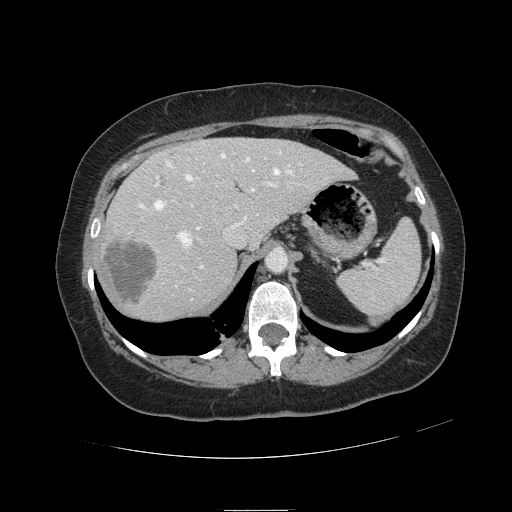
Contrast-enhanced abdominal CT, one axial slice; 120 kVp; intravenous contrast given; soft-tissue window (W 400 / L 40 HU); 2.5 mm slice thickness; 512 × 512 image matrix. Female patient, age 52 years. Case-level facts recorded for this patient, not image findings: diagnosis: colorectal cancer liver metastases, imaged before liver resection; multiple liver metastases: yes; largest metastasis: 6.3 cm; disease in both lobes: no.
Outlined on this slice (expert manual segmentation):
- hepatic veins: box from (x=139, y=151) to (x=301, y=246) px
- liver: (x=100, y=138)–(x=351, y=319)
- planned liver remnant (the part of the liver to remain after resection): (x=168, y=138)–(x=351, y=244)
- portal vein (with intrahepatic branches): (x=155, y=158)–(x=277, y=291)
- liver metastasis: (x=104, y=239)–(x=158, y=305)